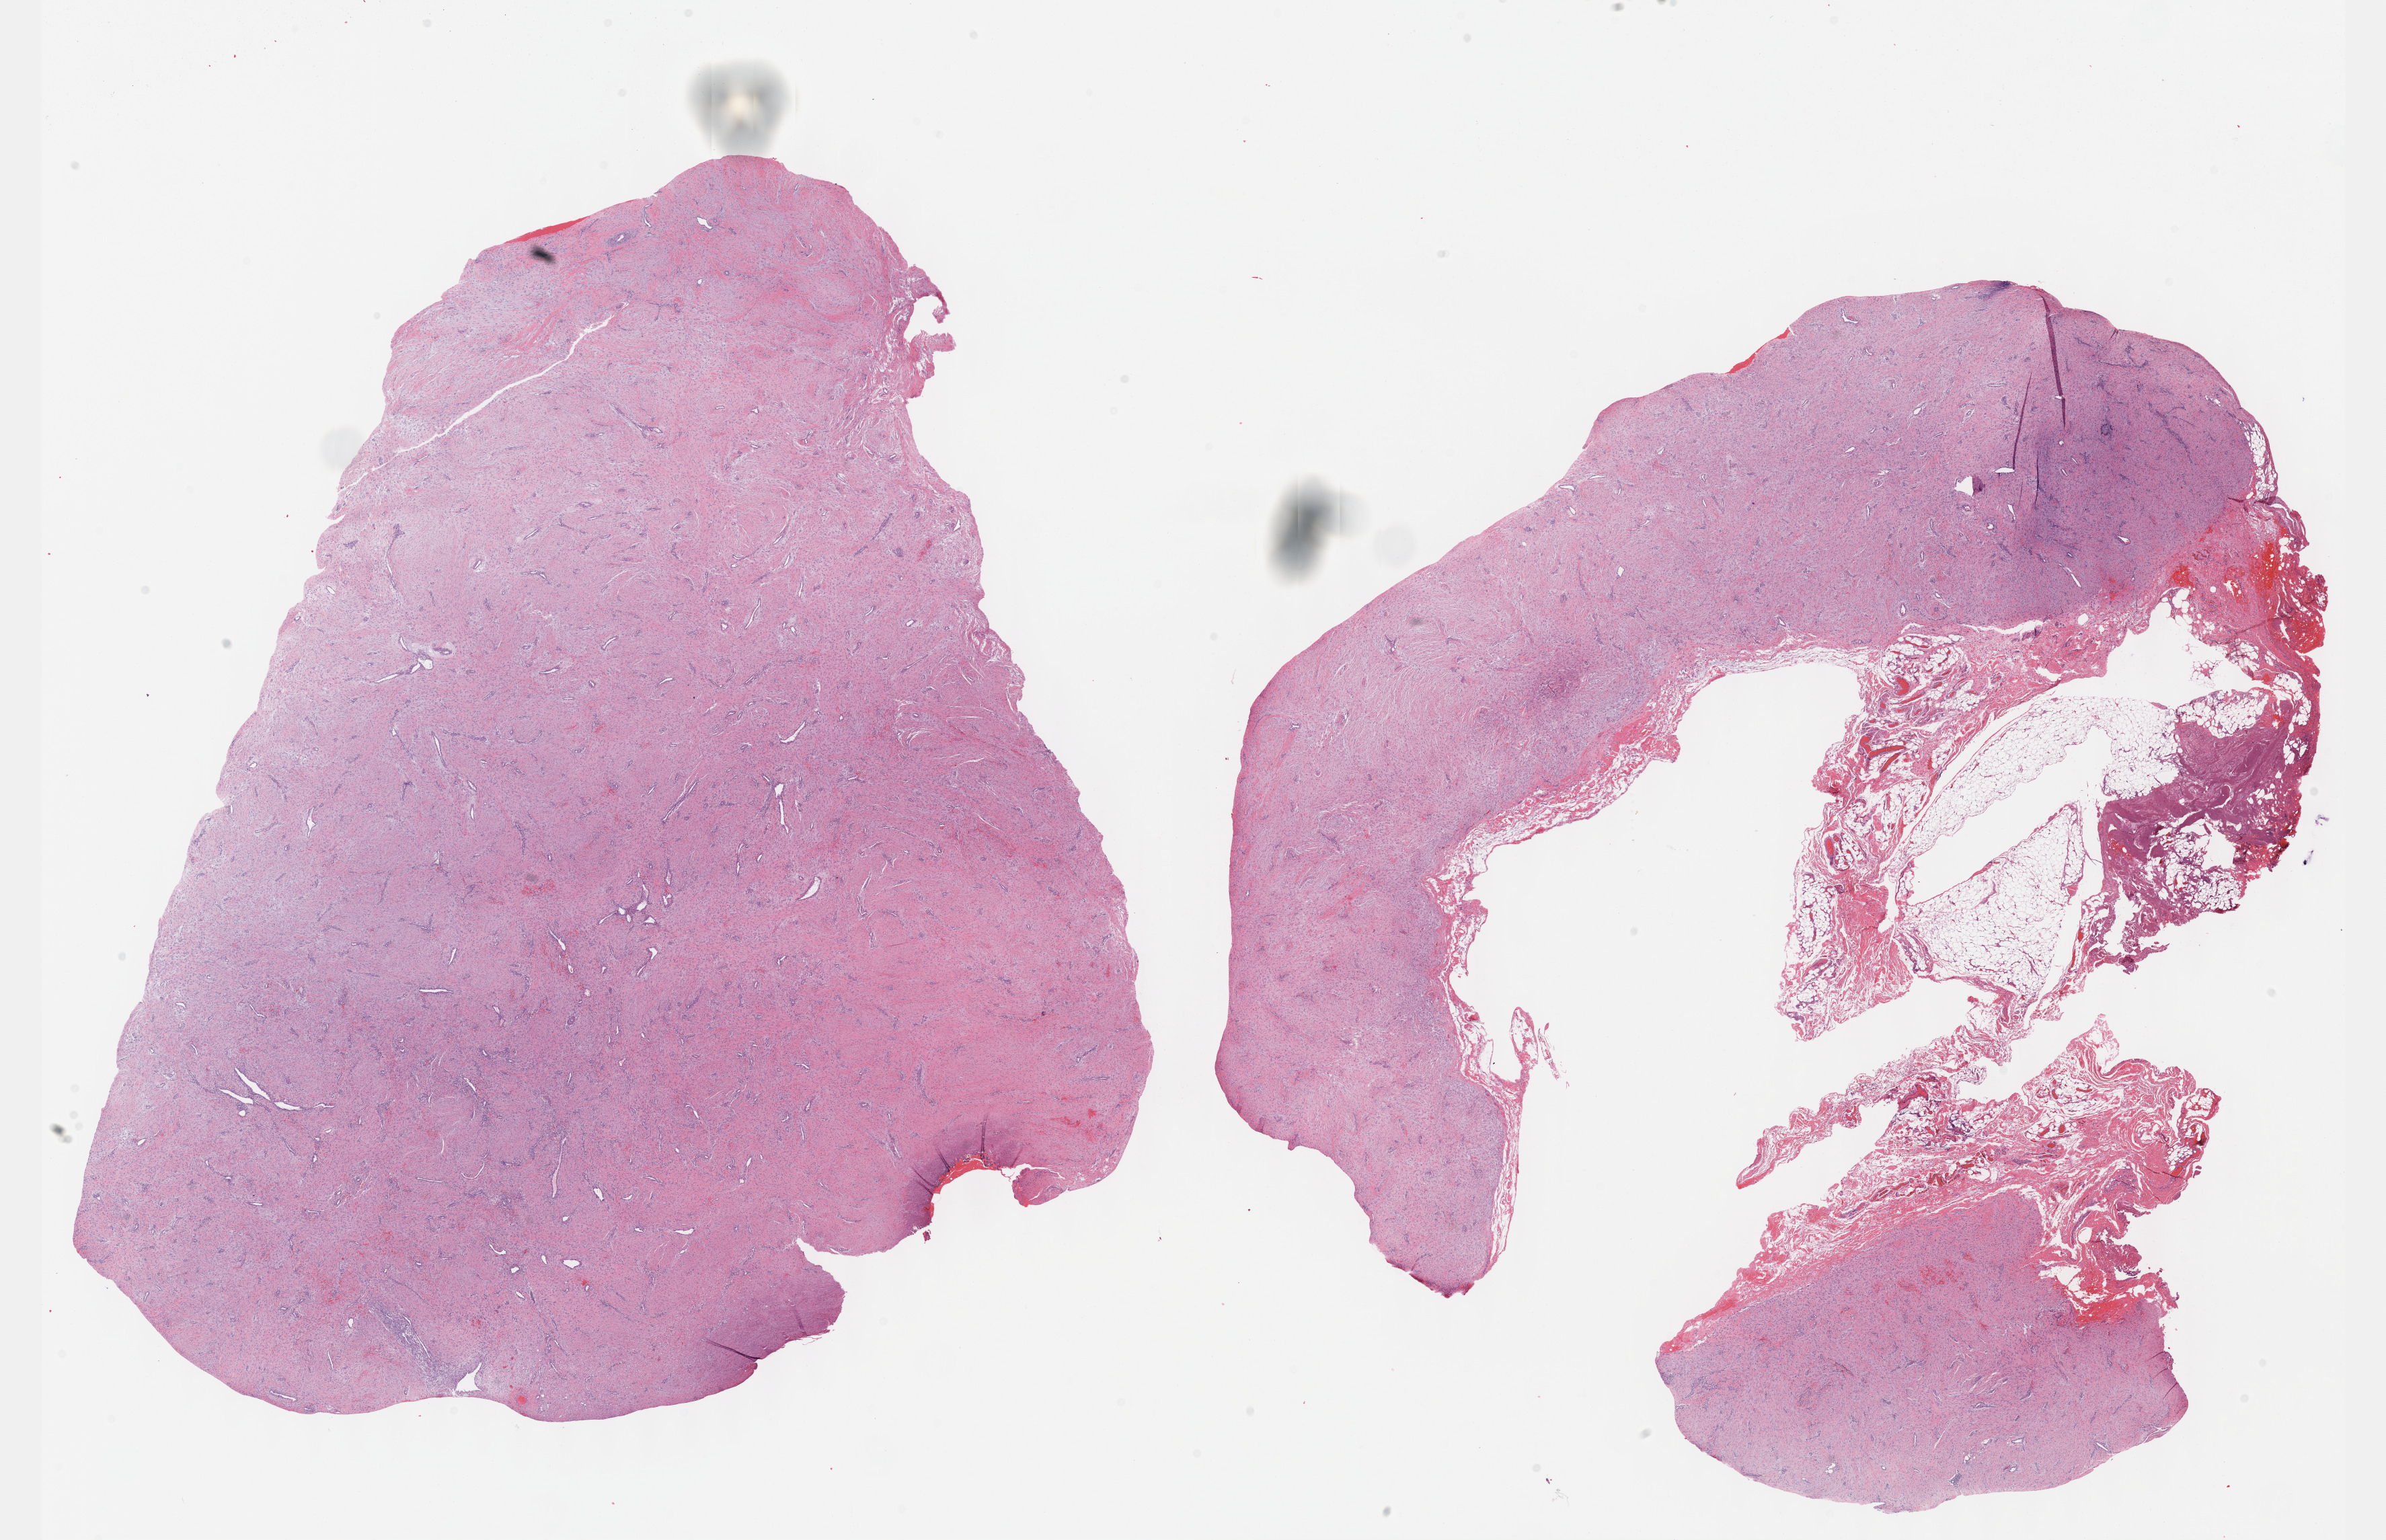
Whole-slide histology image, H&E-stained, a low-resolution overview of the entire scanned area, about 28.7 x 18.5 mm, formalin-fixed paraffin-embedded (FFPE) diagnostic section, primary tumour sample from the retroperitoneum and peritoneum. Male patient; age at initial diagnosis 56 years.
Diagnosis: Abdominal fibromatosis (retroperitoneum).